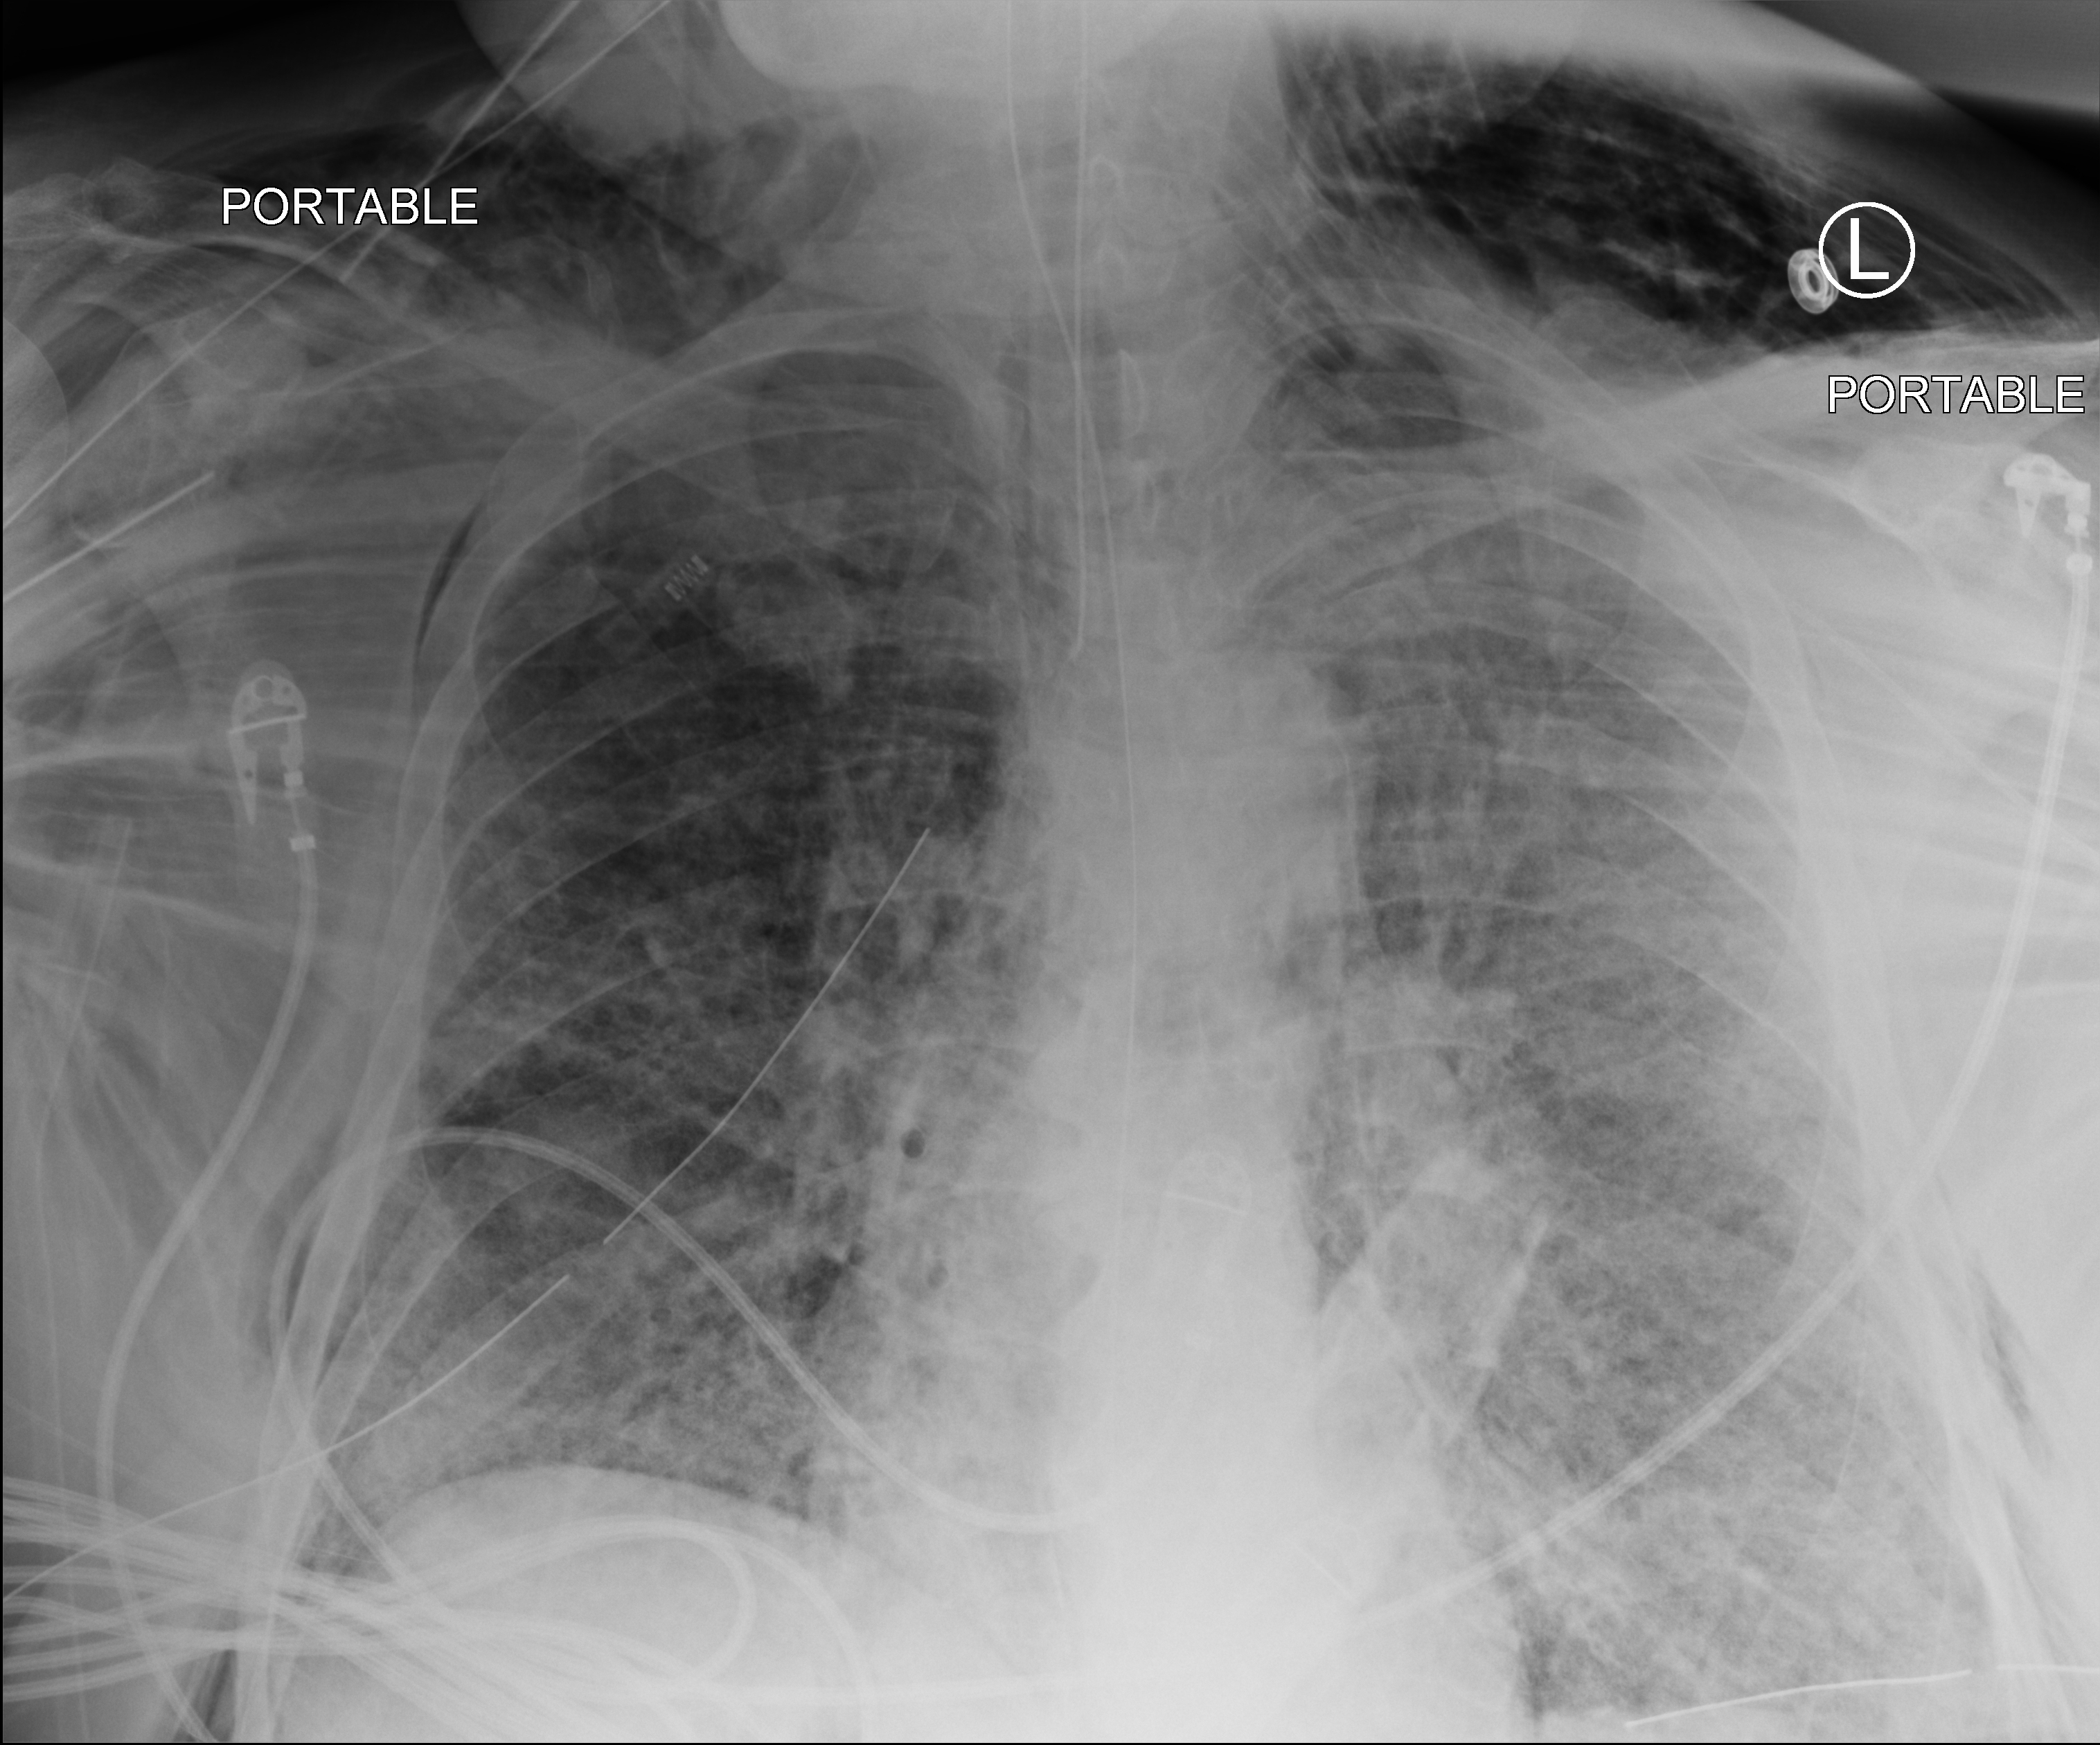
Chest X-ray (portable), anteroposterior (AP) projection. Patient hospitalised with COVID-19, aged 18–59 years.
From the hospital-stay record, not from the radiograph (when in the stay this image was taken is not recorded): diabetes (admission record): no; hypertension (admission record): yes; mechanically ventilated during this hospital stay: yes.